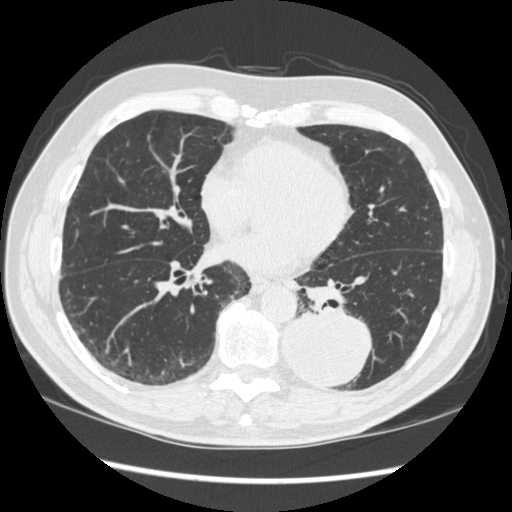
Low-dose screening chest CT, one axial slice. Position 136 of 348 along the scan axis. Reconstruction kernel STANDARD. 120 kVp. Lung window (W 1500 / L -600 HU). 1.25 mm slice thickness. 512 × 512 image matrix.
Annotated regions visible in this slice (outlined manually by an expert reader):
- lesion 1 (tumor, lower lobe of left lung): bounding box [x1, y1, x2, y2] px = [283, 309, 372, 387]